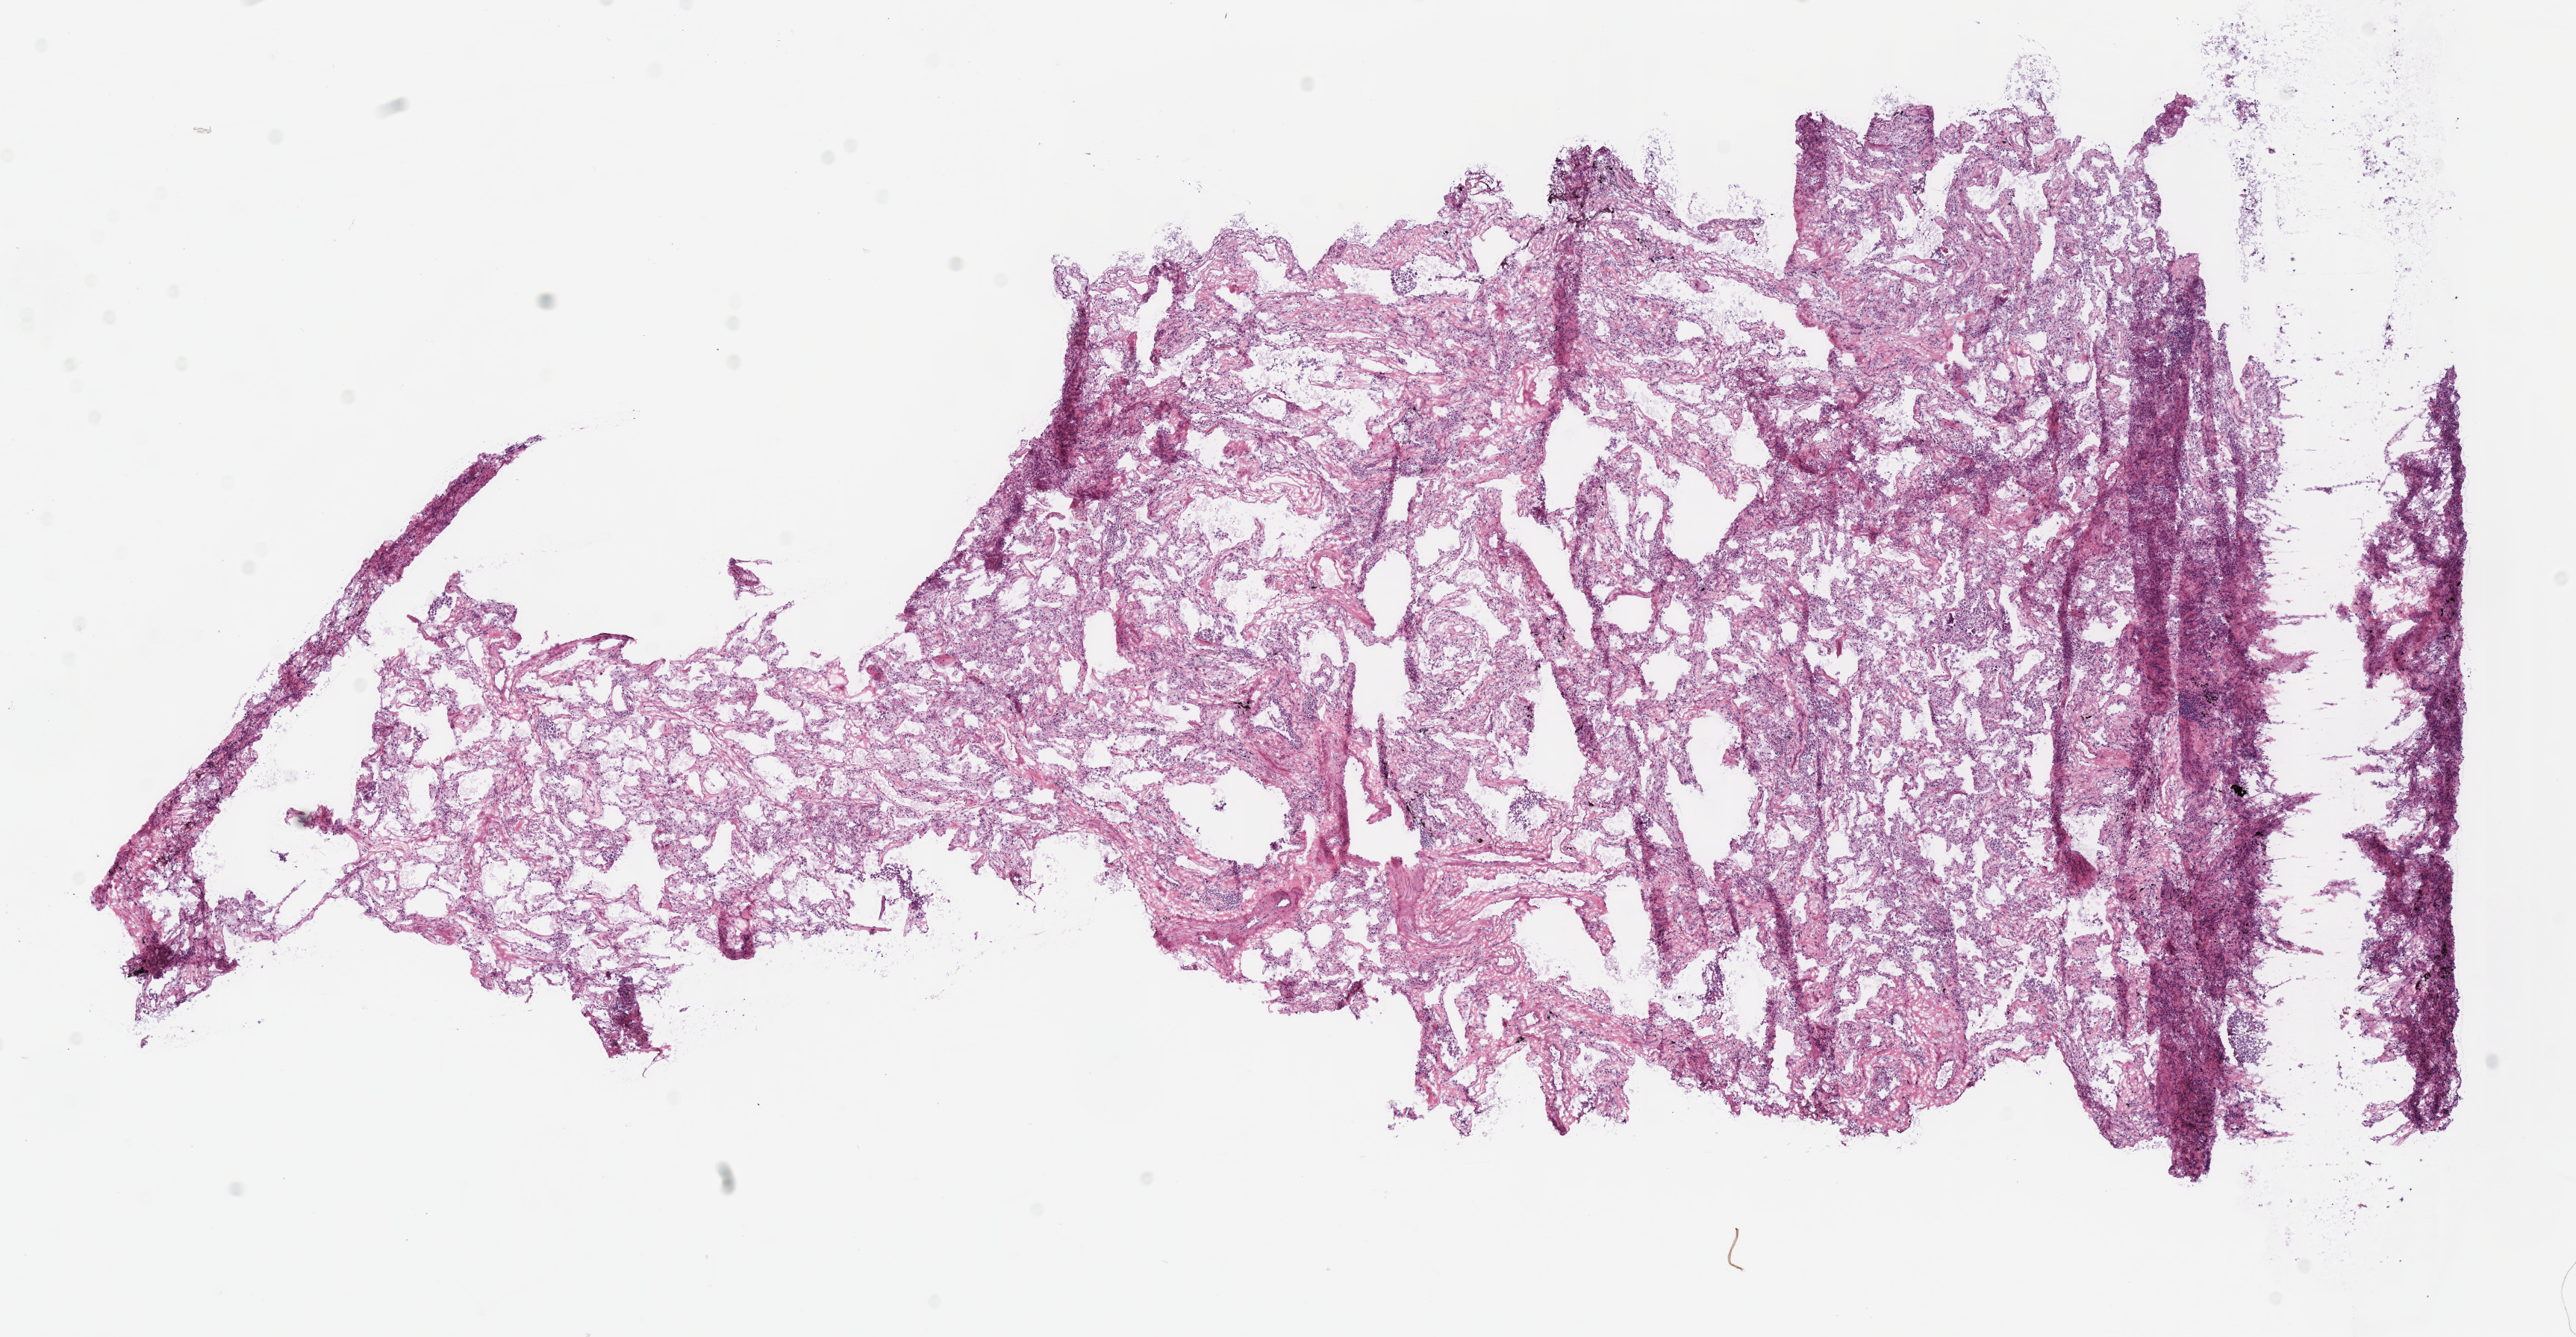
Whole-slide histology image, H&E, whole scanned area (about 13.6 x 7.1 mm, slide scanned at 40x) shown as a low-resolution overview; frozen section from the top of the tissue portion; sample: solid tissue normal (non-tumour tissue), lung. Female patient; age at initial diagnosis 58 years.
This section: solid tissue normal (non-tumour) sample from the same patient. Patient diagnosis: Squamous cell carcinoma, NOS (upper lobe, lung).